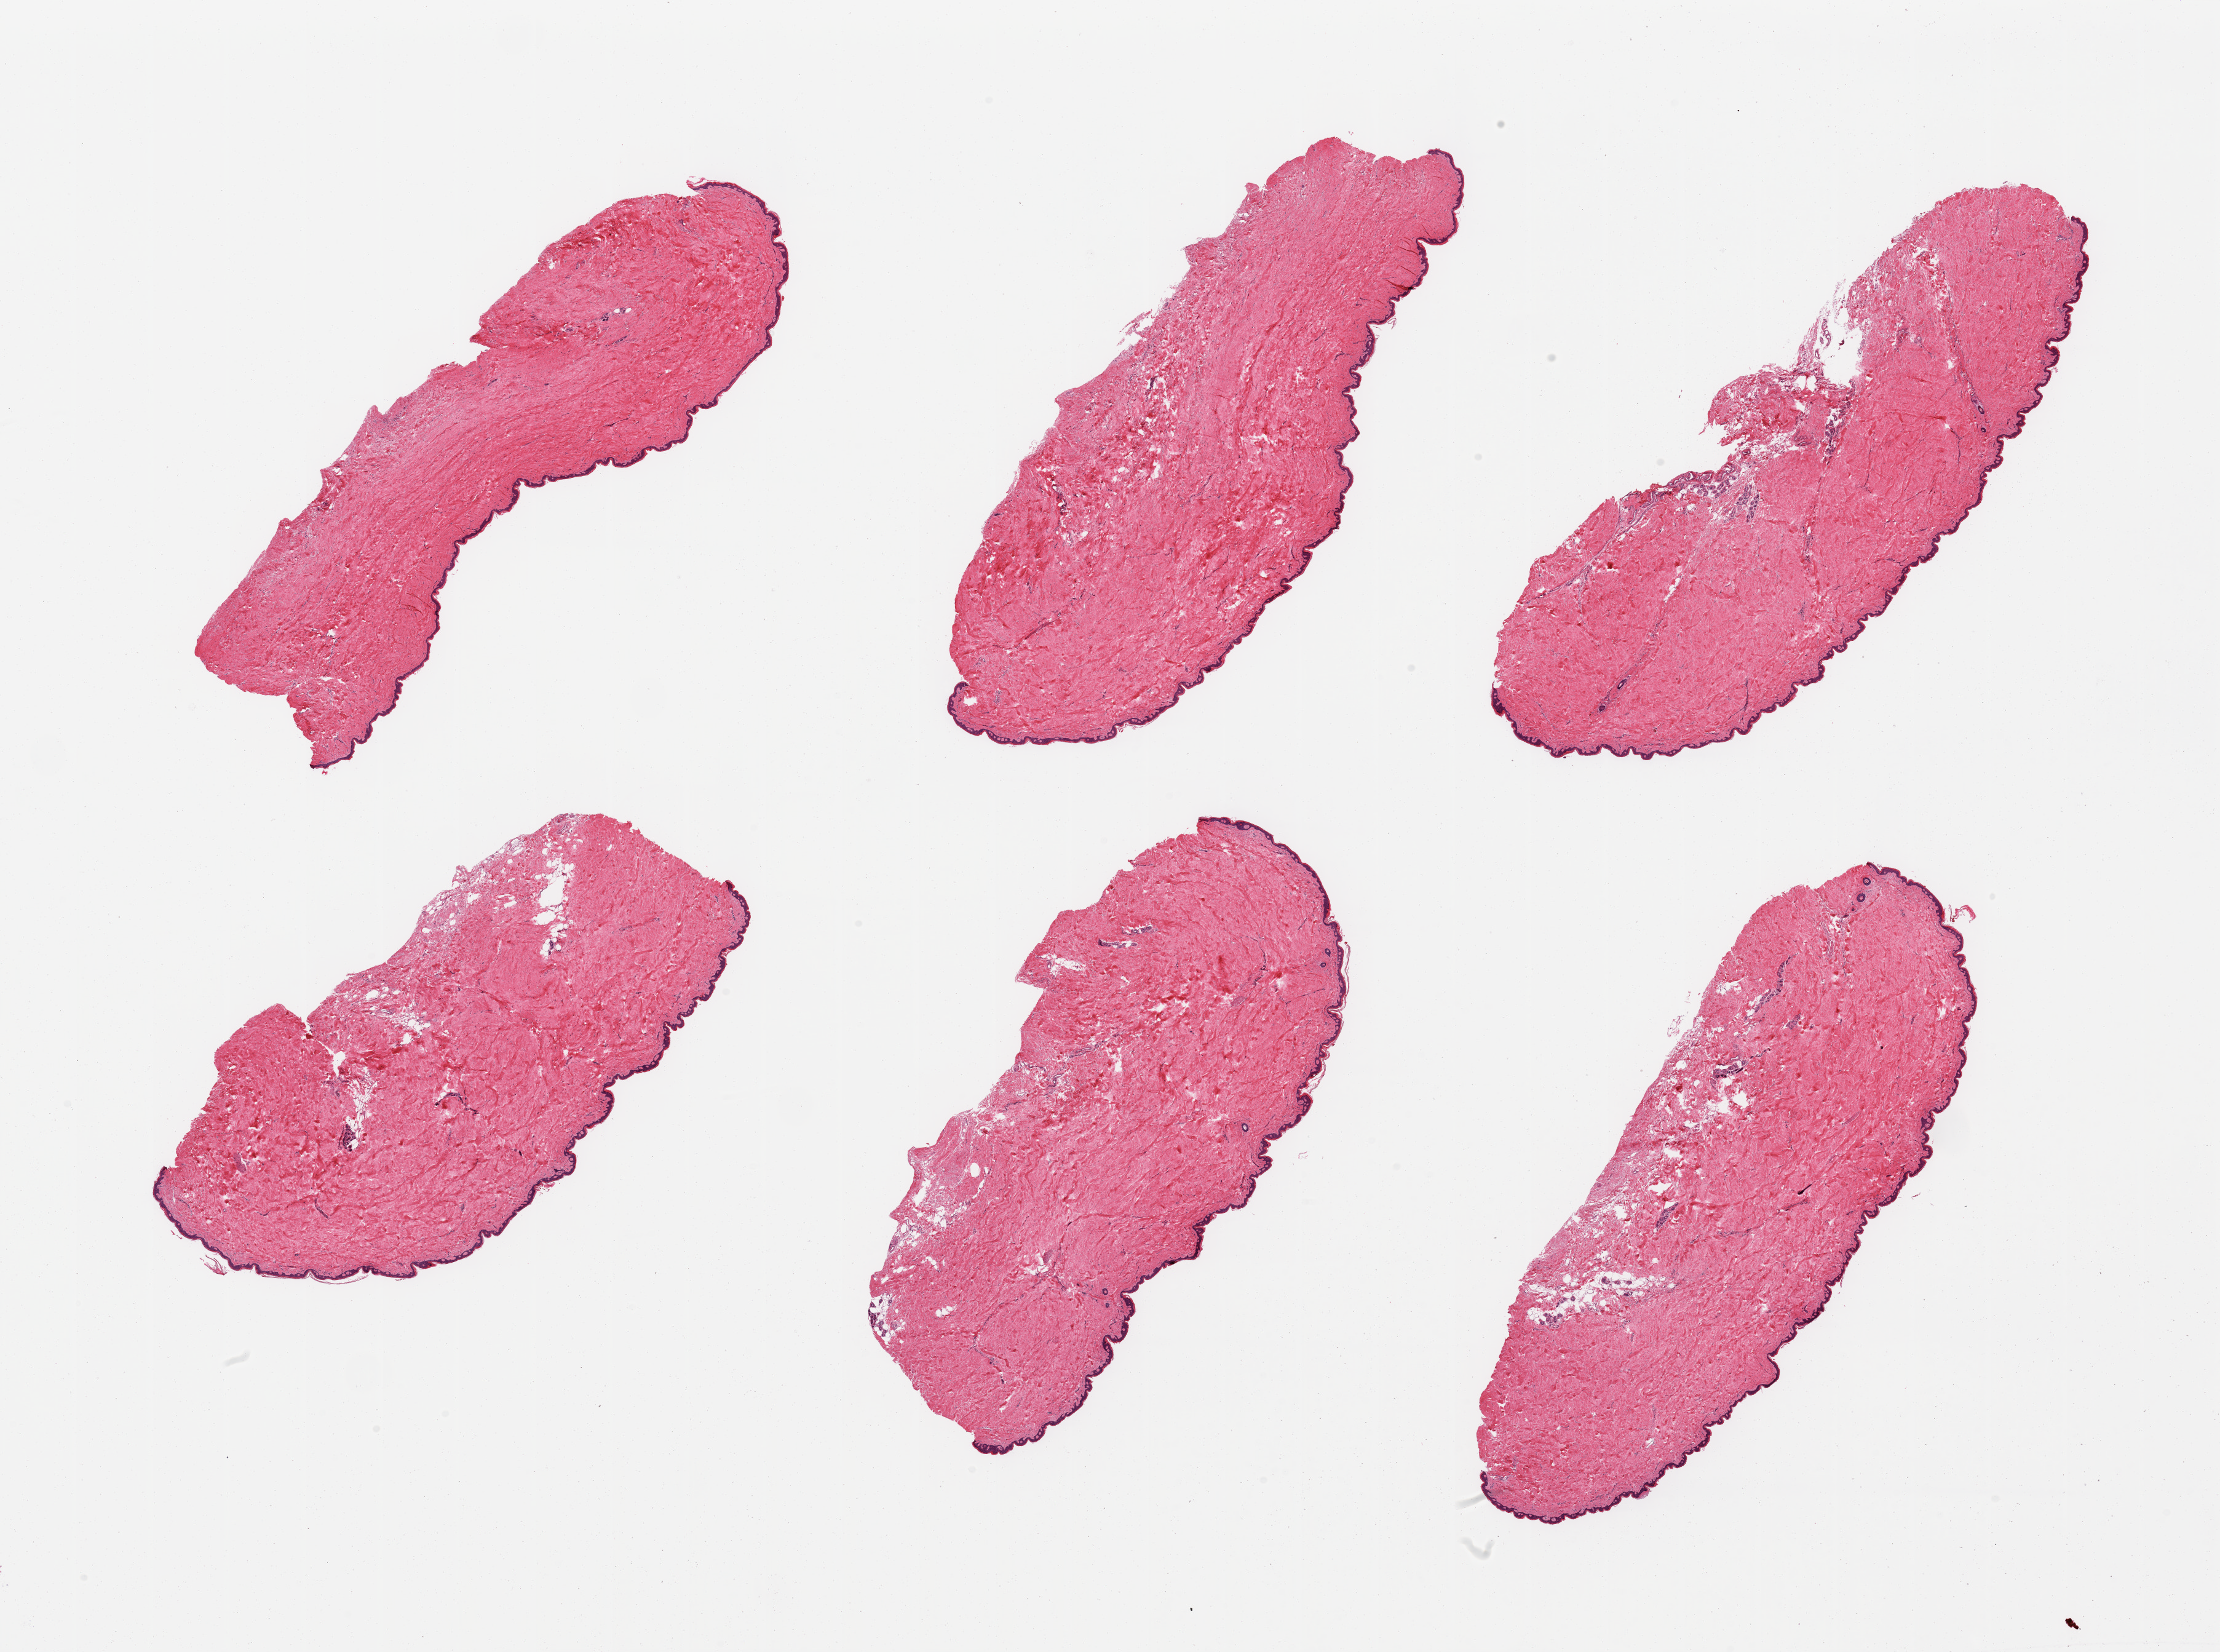
Whole-slide image, haematoxylin and eosin stain — a low-resolution overview of the entire scanned area, about 28.5 x 21.2 mm (from a 20x scan); PAXgene-fixed, paraffin-embedded tissue; section of skin of suprapubic region (target tissue); donor tissue sample. Donor sex: female.
* reviewer comment on this tissue sample: 6 pieces, no dermal fat; squamous epithelium is ~50 microns